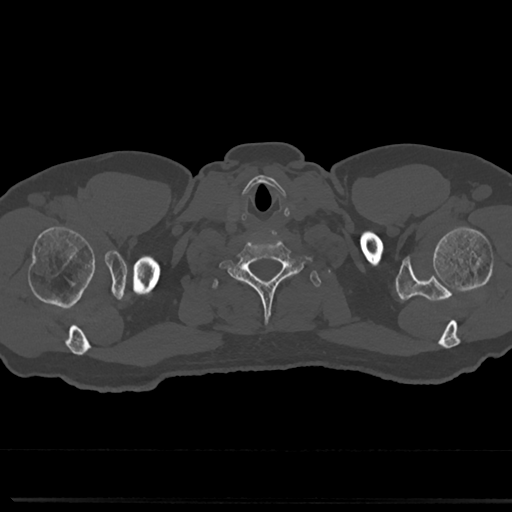
CT including the spine, one axial slice. Slice 702 of 817 in the series (ordered by position). Bone window (W 1800 / L 400 HU). 512 × 512 image matrix, field of view 355 × 355 mm. Patient: male, 61 years. Case-level facts recorded for this patient, not image findings: primary cancer: prostate.
Annotated regions visible in this slice (semi-automatic segmentation, software-assisted and operator-edited):
- T1 vertebra: bounding box <209,273,317,296> (left, top, right, bottom; pixels)